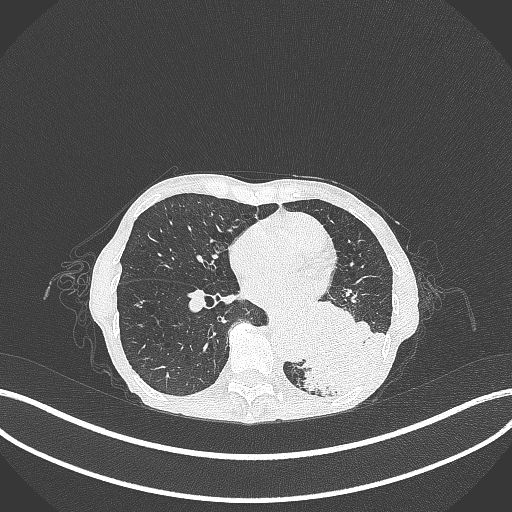
Chest CT, one axial slice. Slice 110 of 347 in the series (ordered by position). 120 kVp. Lung window (W 1500 / L -600 HU). 1 mm slice thickness. 512 × 512 image matrix, field of view 400 × 400 mm. Patient: female, 70 years. From the clinical record (not read from this slice): clinical TNM (as recorded): T3 N0 M0.
Outlined on this slice (rectangle marked by the reading radiologist):
- lung tumour (recorded histology: small cell carcinoma): box from (x=294, y=309) to (x=393, y=401) px